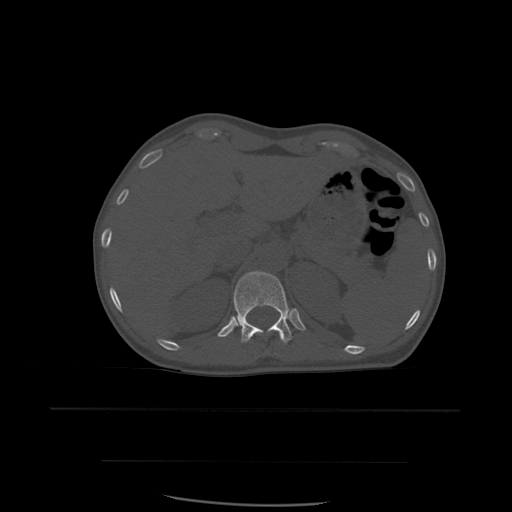
CT including the spine, one axial slice. Slice 275 of 574 in the series (ordered by position). Bone window (W 1800 / L 400 HU). 1.25 mm slice thickness. 512 × 512 image matrix. Patient age 48 years. From the clinical record (not read from this slice): primary cancer: lung; vertebrae with lytic lesions (as recorded): T11.
Structures marked on this image (semi-automatic segmentation, software-assisted and operator-edited):
- T12 vertebra: bounding box (x1, y1, x2, y2) in pixels: (234, 271, 293, 344)